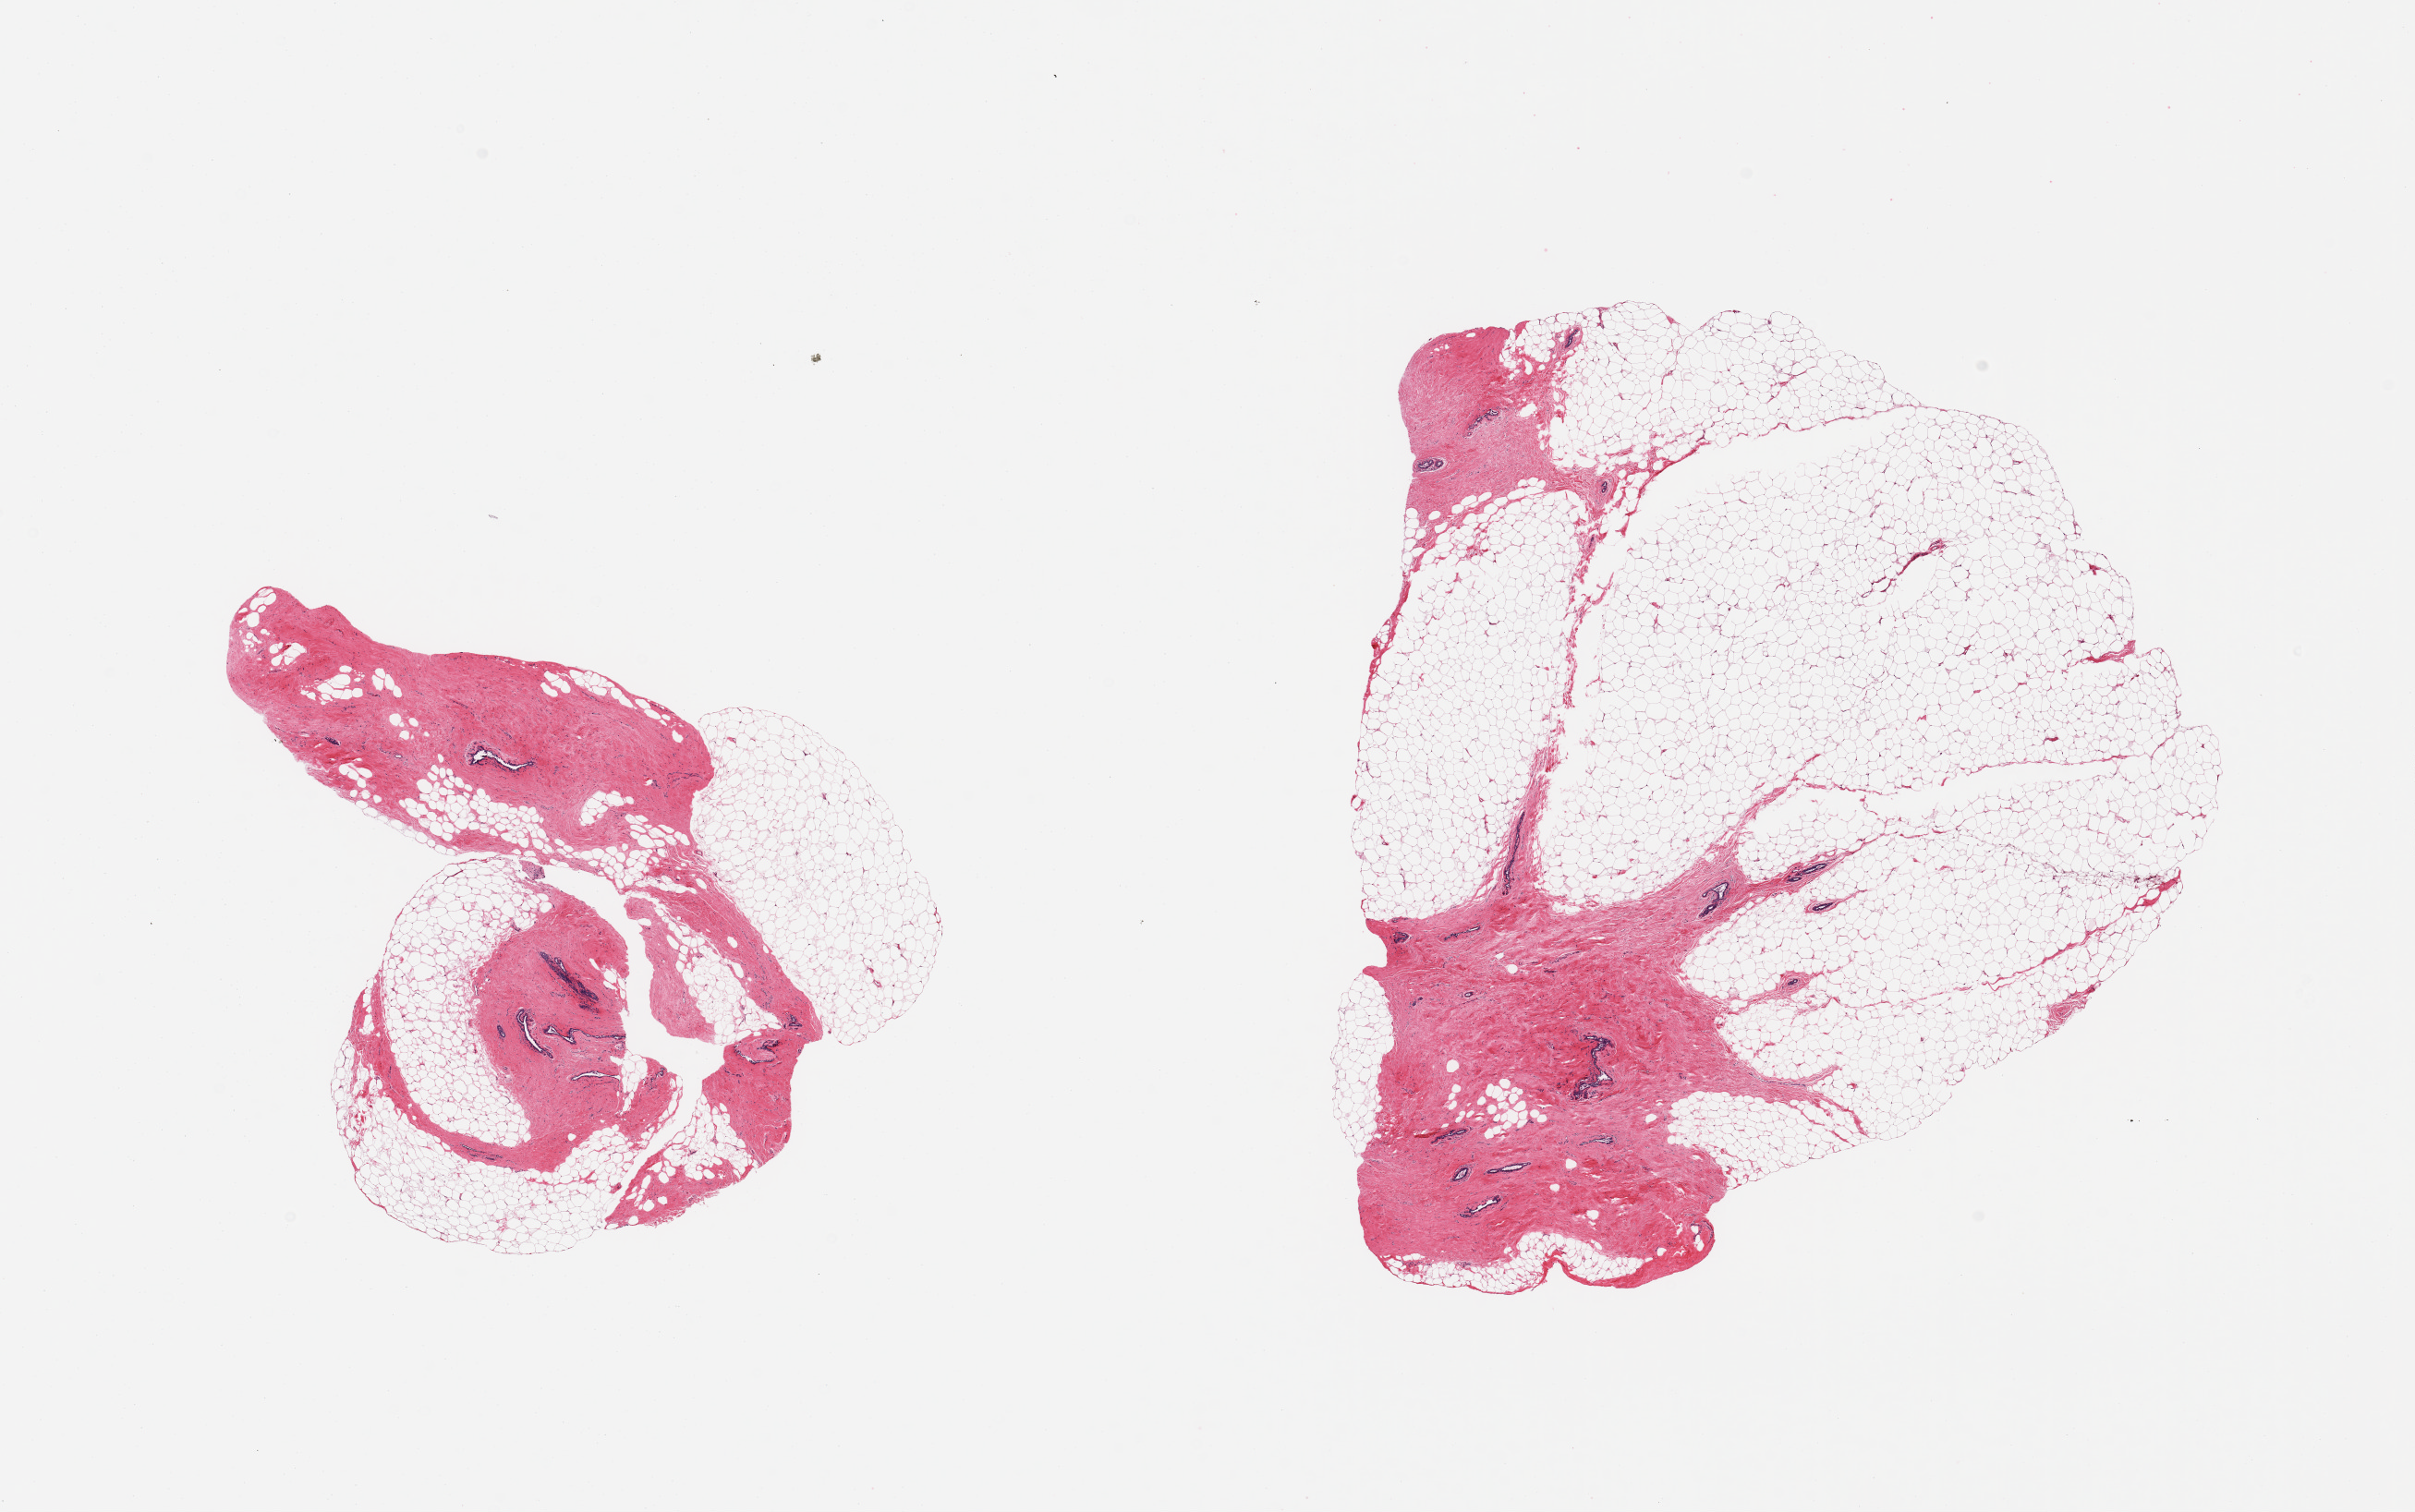
Digitized hematoxylin and eosin (H&E)-stained section, brightfield — whole scanned area (about 20.7 x 12.9 mm, slide scanned at 20x) shown as a low-resolution overview, PAXgene-fixed paraffin-embedded (PFPE) section, section of breast (target tissue), tissue donor sample. Male donor.
Pathologist's review note for this sample: 2 pieces; mature adipose tissue with 30 and 50% dense fibrocollagenous stroma with scattered ducts.